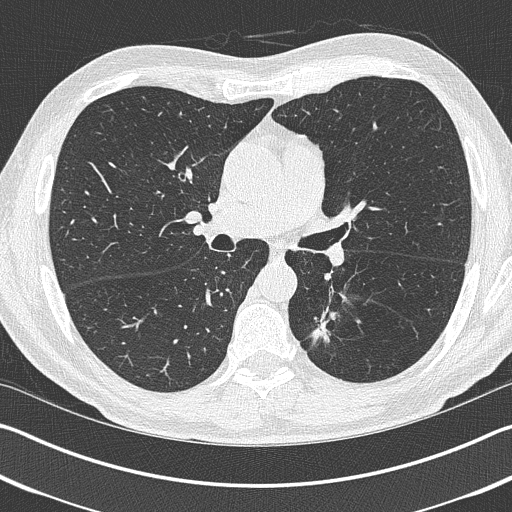
Low-dose screening chest CT, one axial slice; position 240 of 402 along the scan axis; reconstruction kernel B50f; lung window (W 1500 / L -600 HU); 512 × 512 image matrix.
Annotated regions visible in this slice (expert manual segmentation):
- lesion 1 (tumor, lower lobe of left lung): bounding box <310,312,339,344> (left, top, right, bottom; pixels)